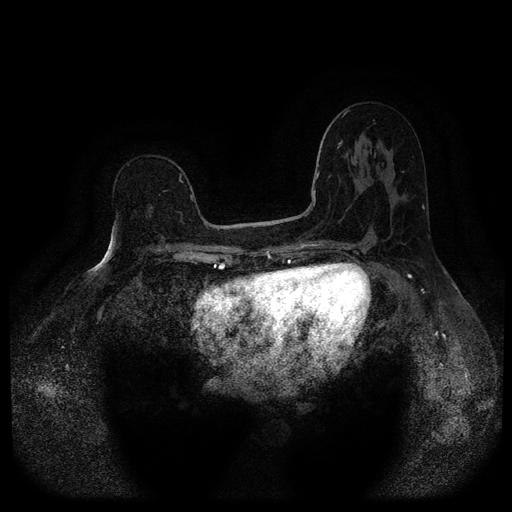
Breast MRI (dynamic contrast-enhanced, multi-phase), one axial slice; dynamic contrast-enhanced series, time point 2 of 5 at this slice position (early post-contrast); 1.5 T; TE 2.6 ms, TR 5.4 ms; 2 mm slice thickness; 512 × 512 image matrix, field of view 340 × 340 mm. Patient: female, 64 years.
Annotated regions visible in this slice (semi-automatically segmented with operator editing):
- breast lesion (labelled benign in the annotation): bounding box [x1, y1, x2, y2] px = [155, 233, 167, 247]